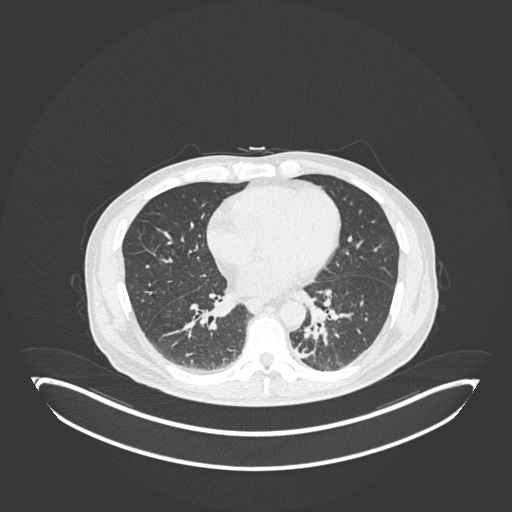
Chest CT, one axial slice; position 63 of 251 along the scan axis; lung window (W 1500 / L -600 HU); 1 mm slice thickness; 512 × 512 image matrix. Patient: male, 72 years. From the clinical record (not read from this slice): clinical TNM (as recorded): T2b N0 M1.
Outlined on this slice (rectangle marked by the reading radiologist):
- lung tumour (recorded histology: adenocarcinoma): bounding box <298,321,324,362> (left, top, right, bottom; pixels)